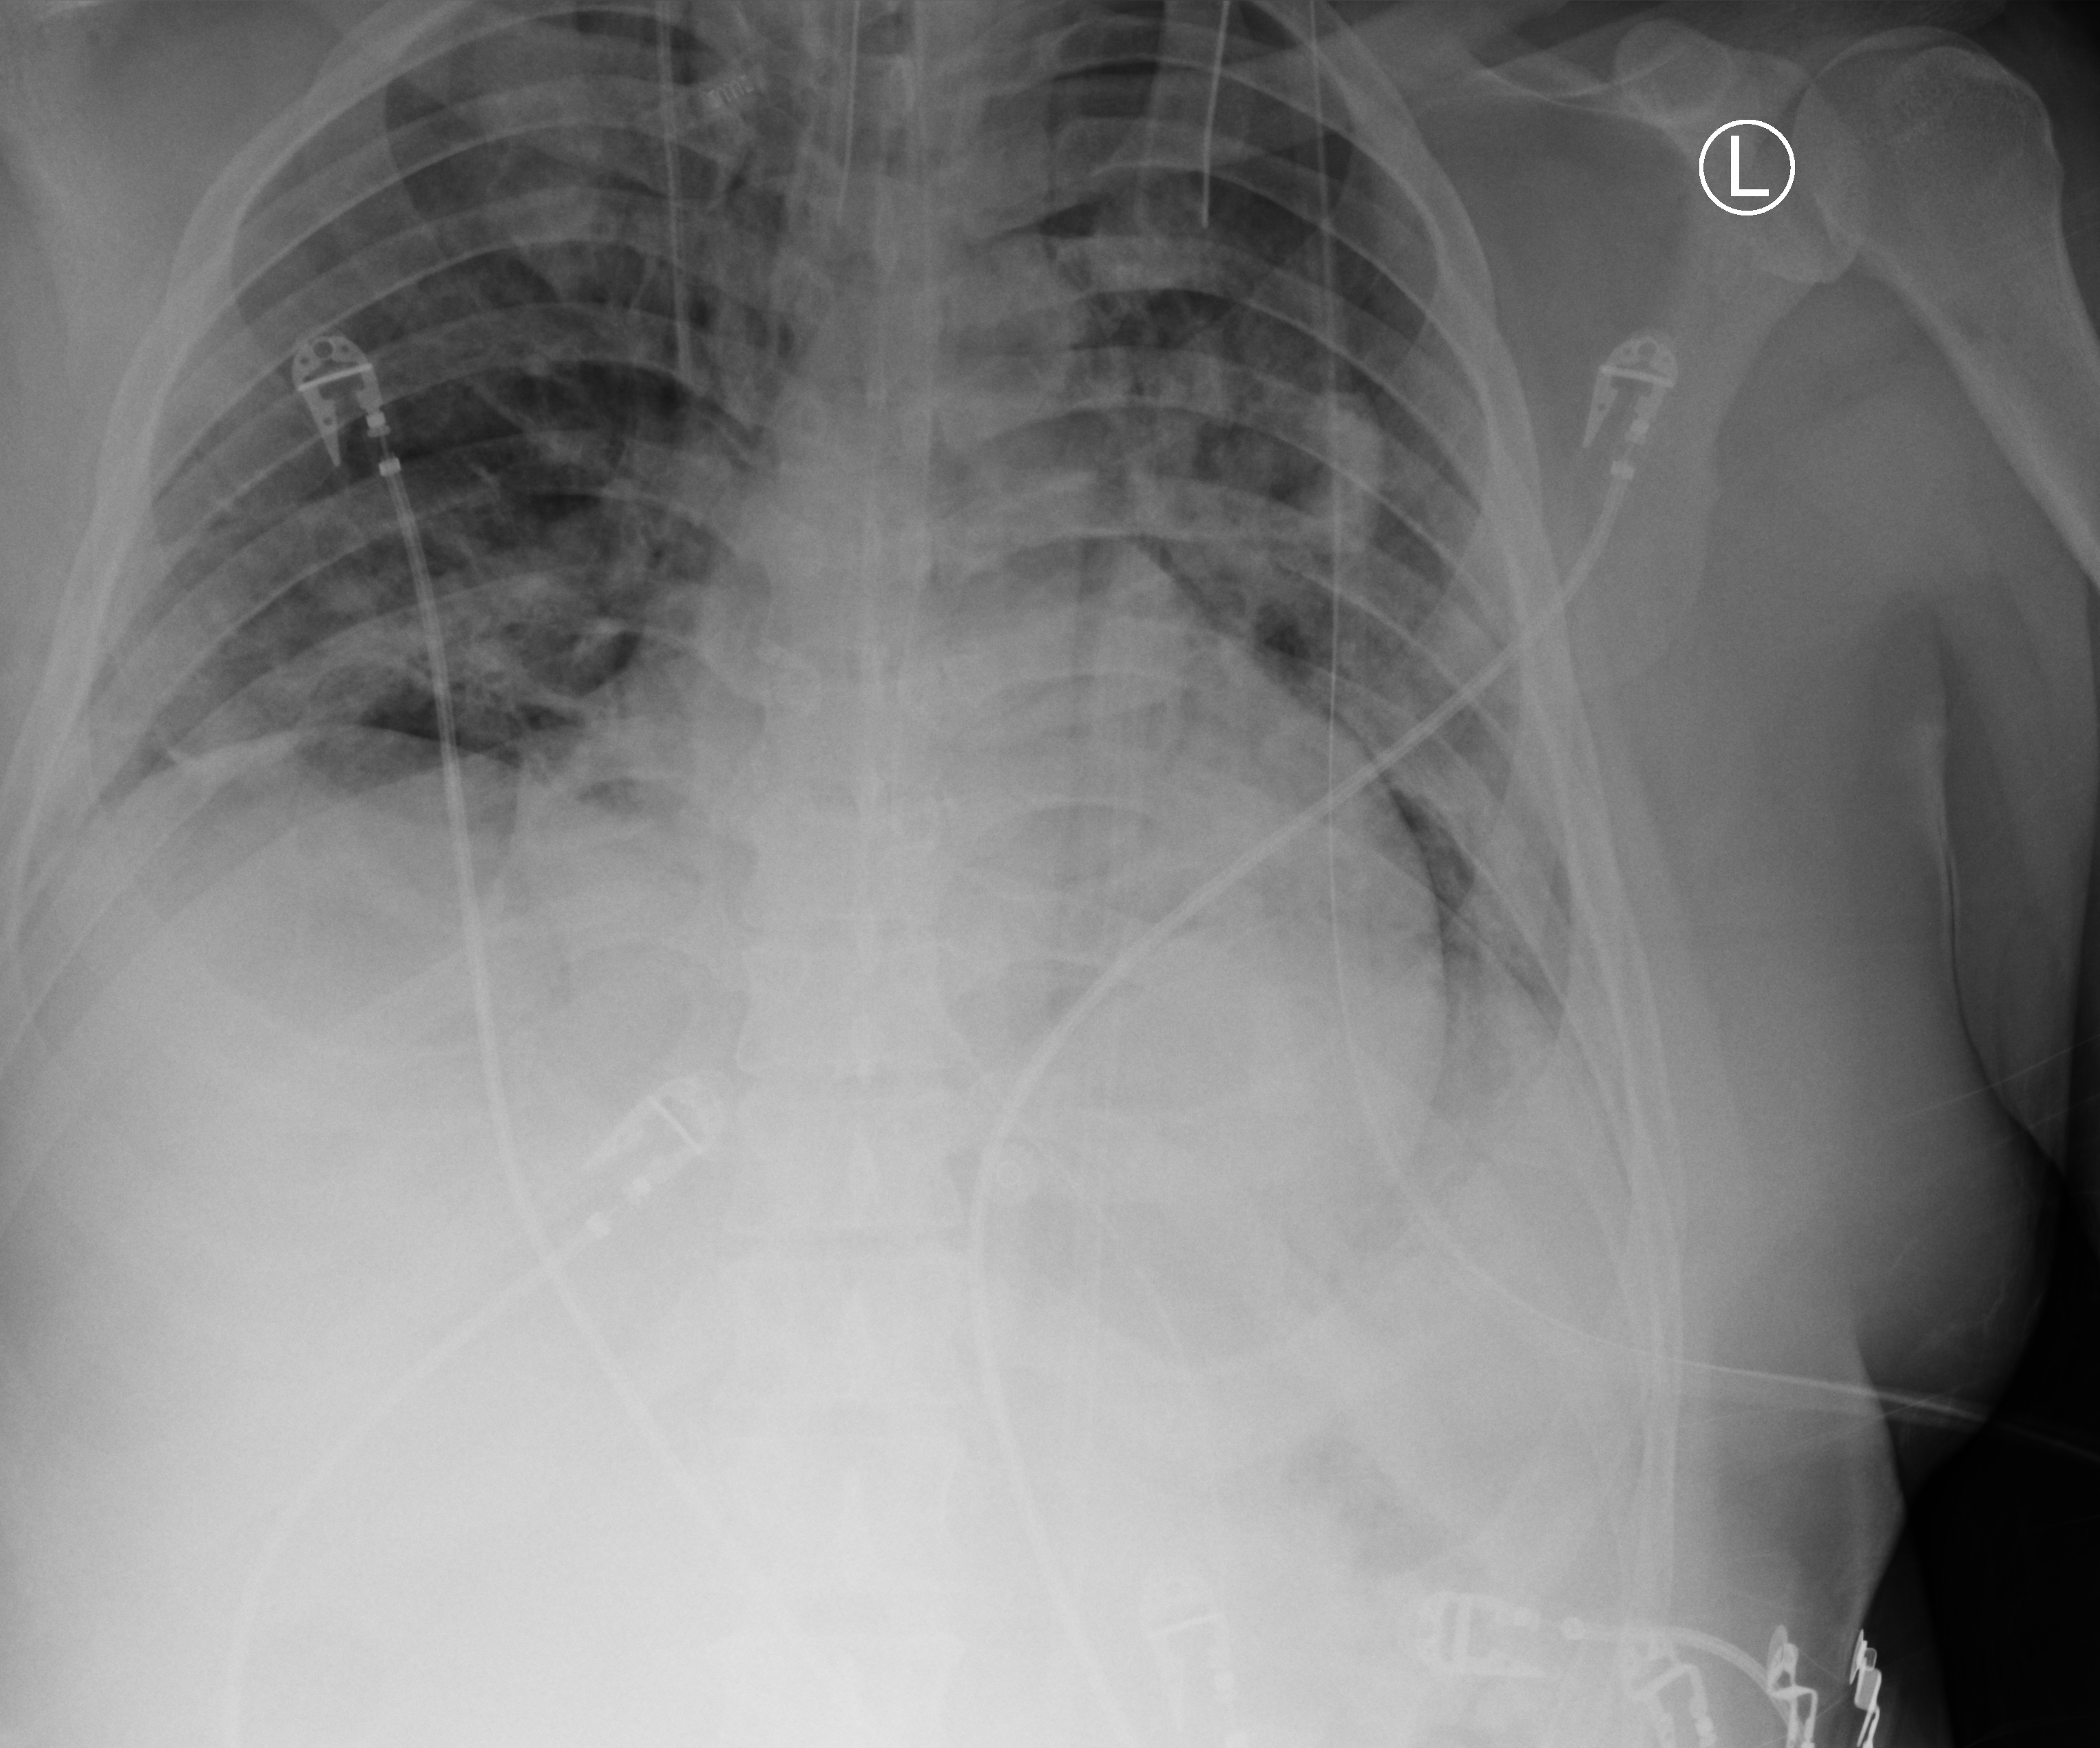
Chest X-ray (portable), anteroposterior (AP) projection. Male patient hospitalised with COVID-19, age 18–59 years.
Admission-level facts for this patient (not findings on this image; timing relative to this image not recorded):
- admitted to intensive care during this hospital stay: yes
- length of hospital stay: 29 days
- mechanically ventilated during this hospital stay: yes